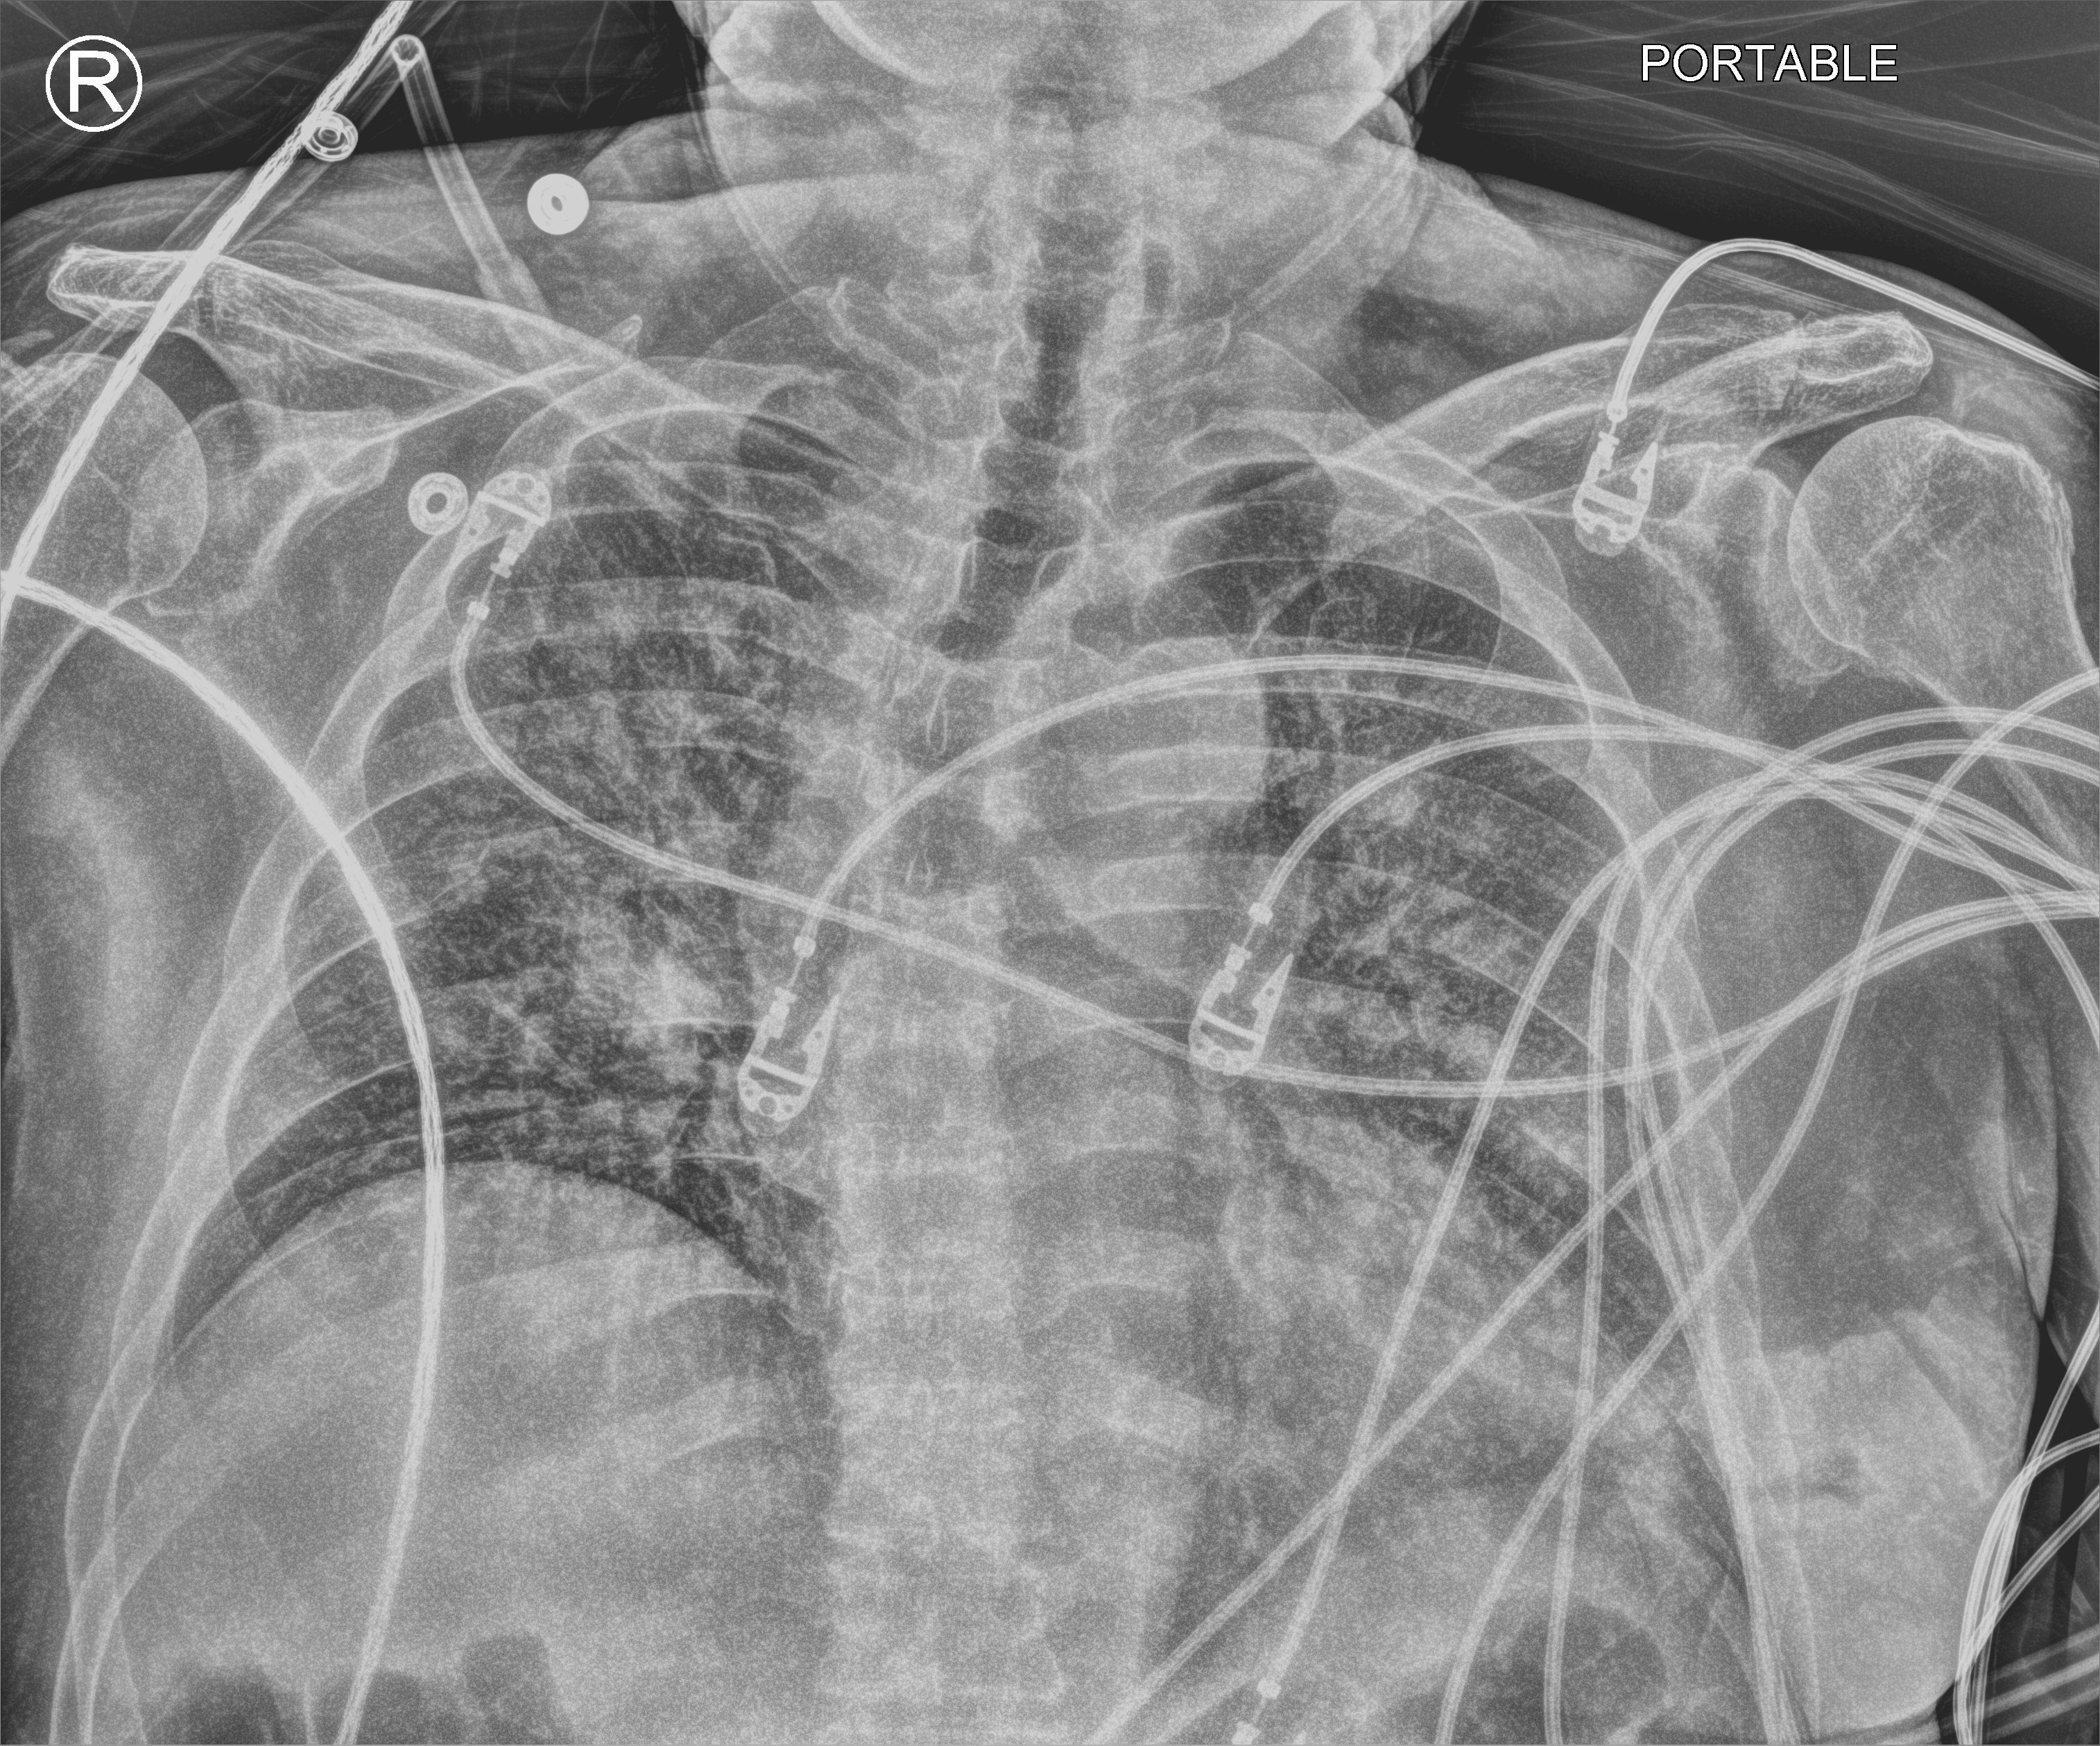
Portable chest radiograph, anteroposterior (AP) projection. Patient hospitalised with COVID-19; male, aged 60–74 years.
Hospital-stay facts (about this admission, not read from this image; timing relative to this image not recorded): mechanically ventilated during this hospital stay: yes.